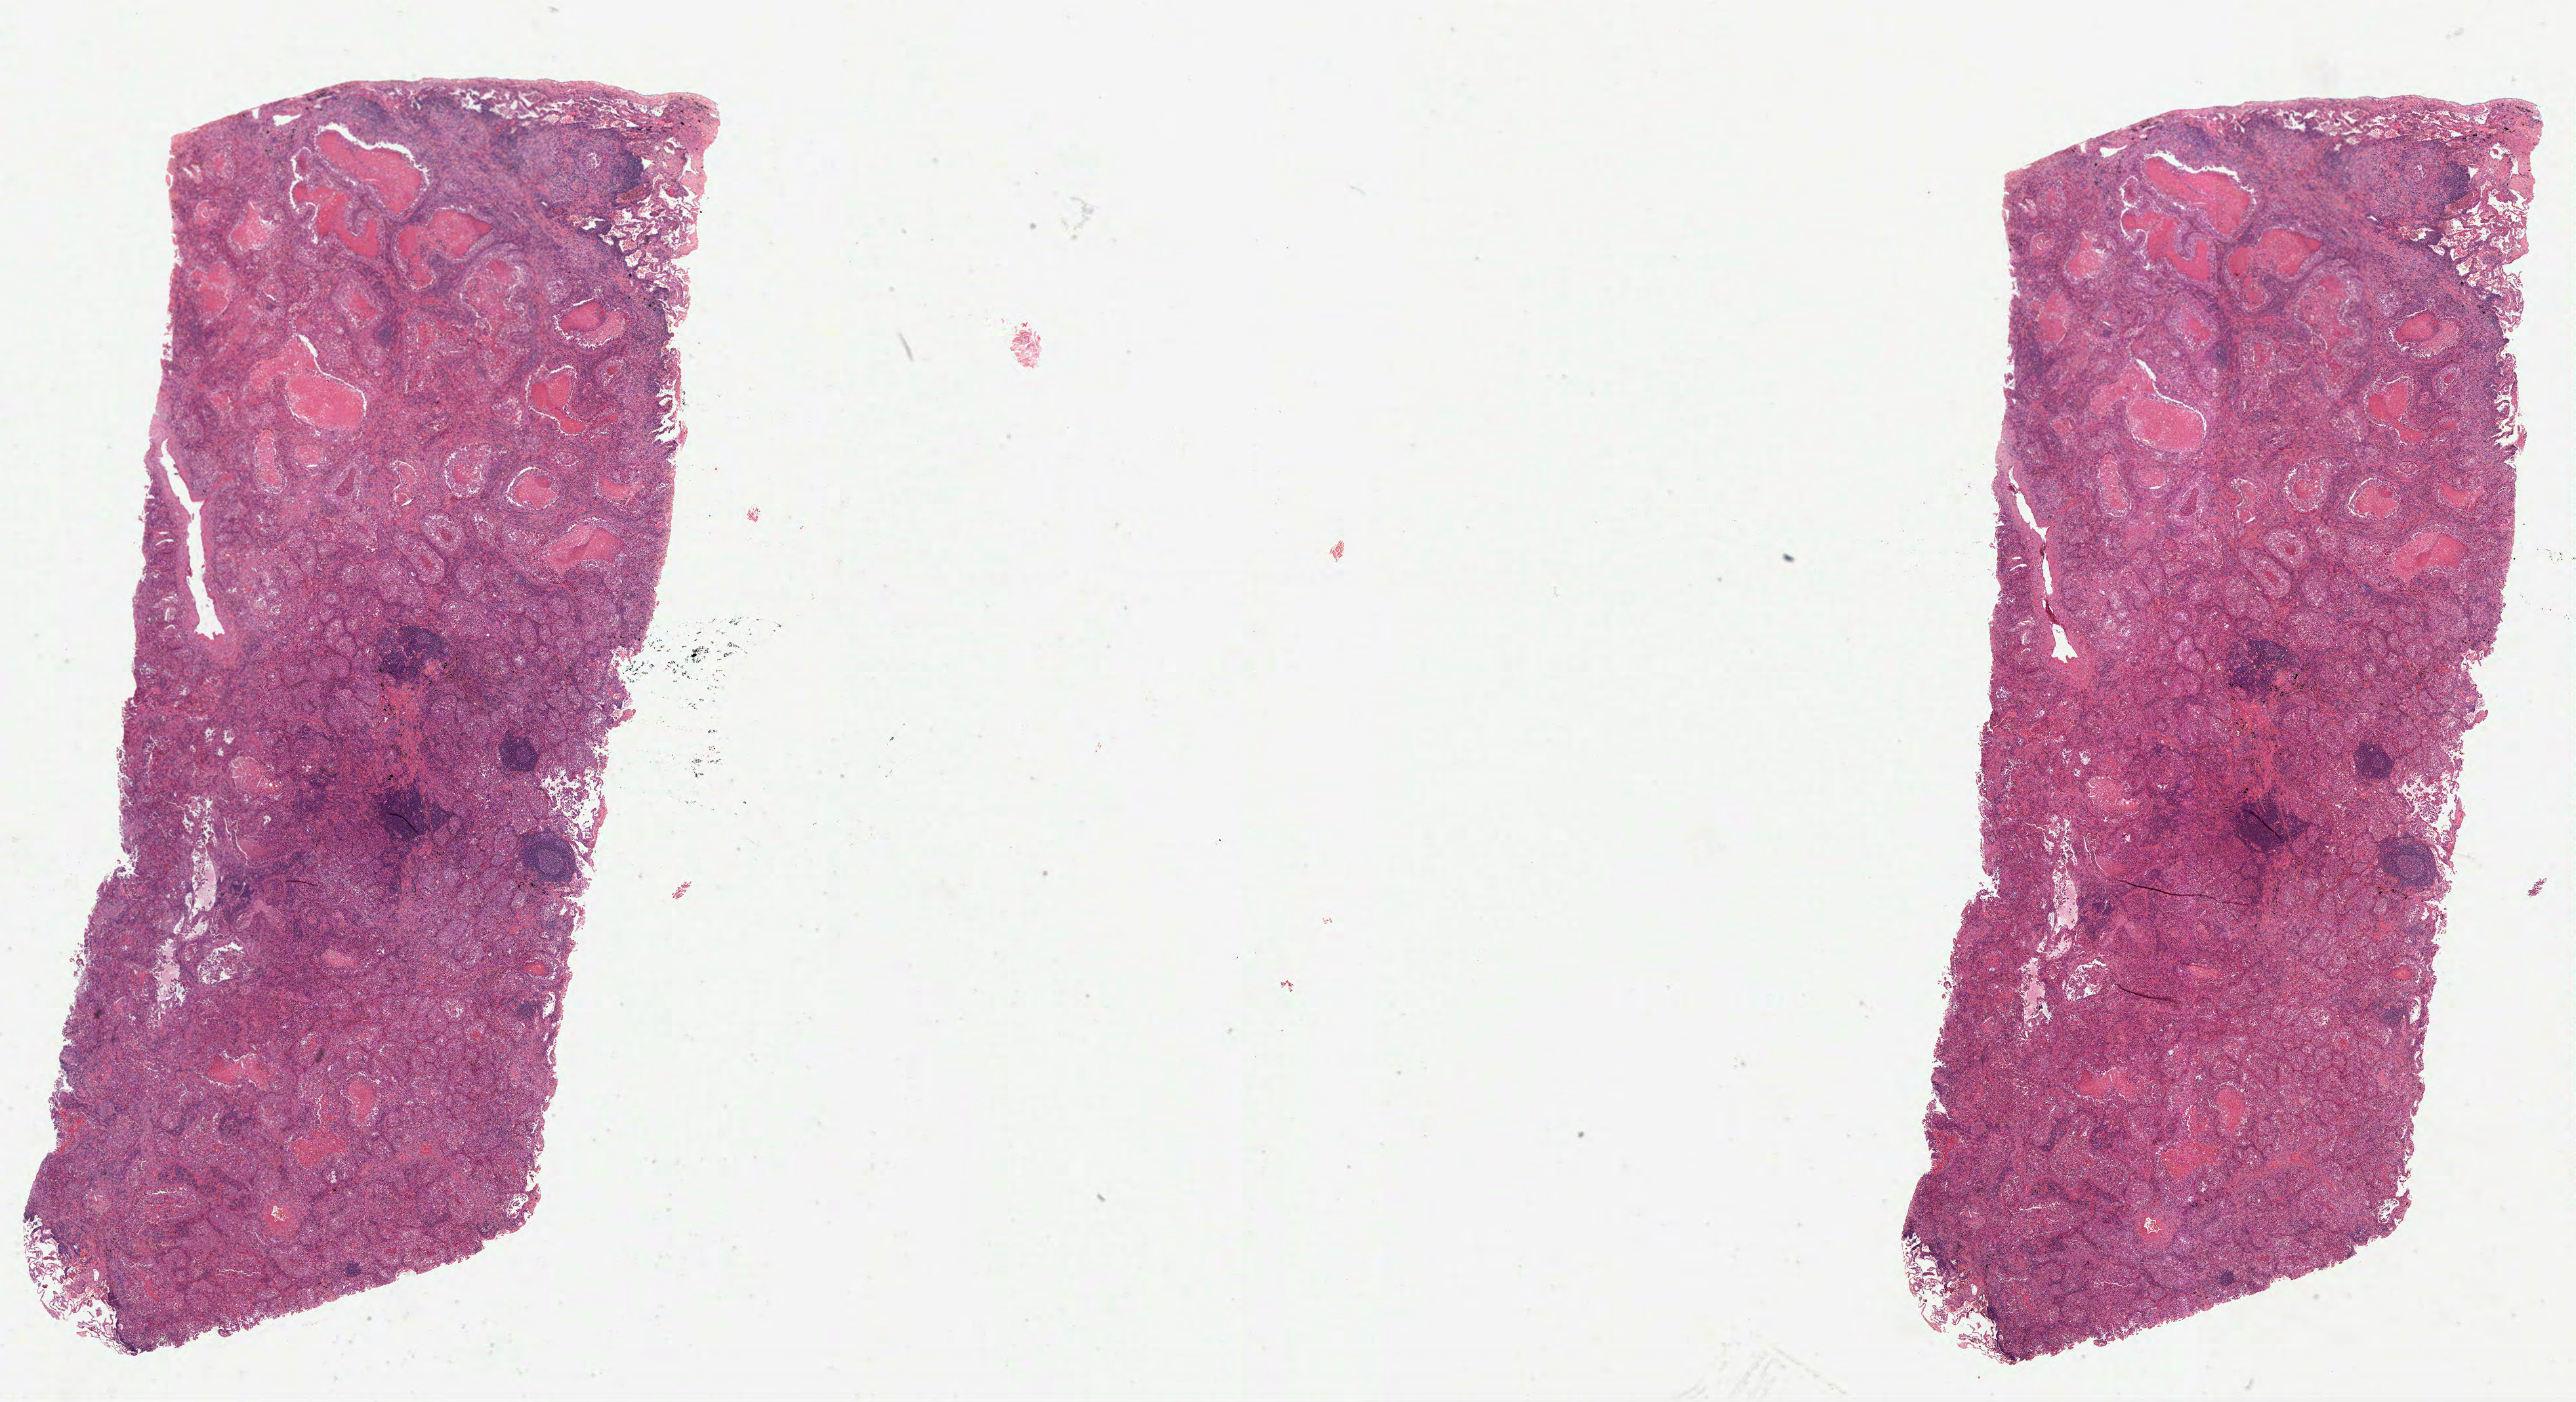
Digitized Hematoxylin and eosin (H&E) stained tissue section (whole slide) — whole scanned area (about 31.7 x 17.2 mm) shown as a low-resolution overview. Formalin-fixed paraffin-embedded (FFPE) diagnostic section. Primary tumour sample from the lung. Female, age 85 years at initial diagnosis.
Diagnosis: Adenocarcinoma, NOS (upper lobe, lung).